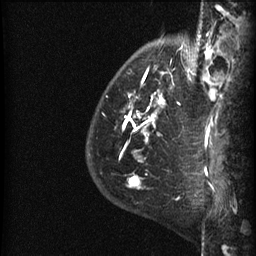
Breast MRI (dynamic contrast-enhanced), one sagittal slice. Slice 11 of 60 in the series (ordered by position). Dynamic contrast-enhanced series, image 2 of 3 at this slice position (ordered by acquisition). 1.5 T. TE 4.2 ms, TR 22.7 ms. 1.5 mm slice thickness. 256 × 256 image matrix, field of view 180 × 180 mm. Female patient, age 48 years. Case-level facts recorded for this patient, not image findings: setting: breast cancer imaged before/during neoadjuvant chemotherapy; receptor status: triple-negative.
Annotated regions visible in this slice (semi-automatic segmentation, software-assisted and operator-edited):
- analysis volume of interest (the breast-tissue region the enhancement analysis was run in; not a lesion): bounding box [x1, y1, x2, y2] px = [89, 35, 191, 180]
- tumour enhancement mask (voxels above the 90 % enhancement threshold inside the analysis volume of interest): [123, 69, 174, 180]